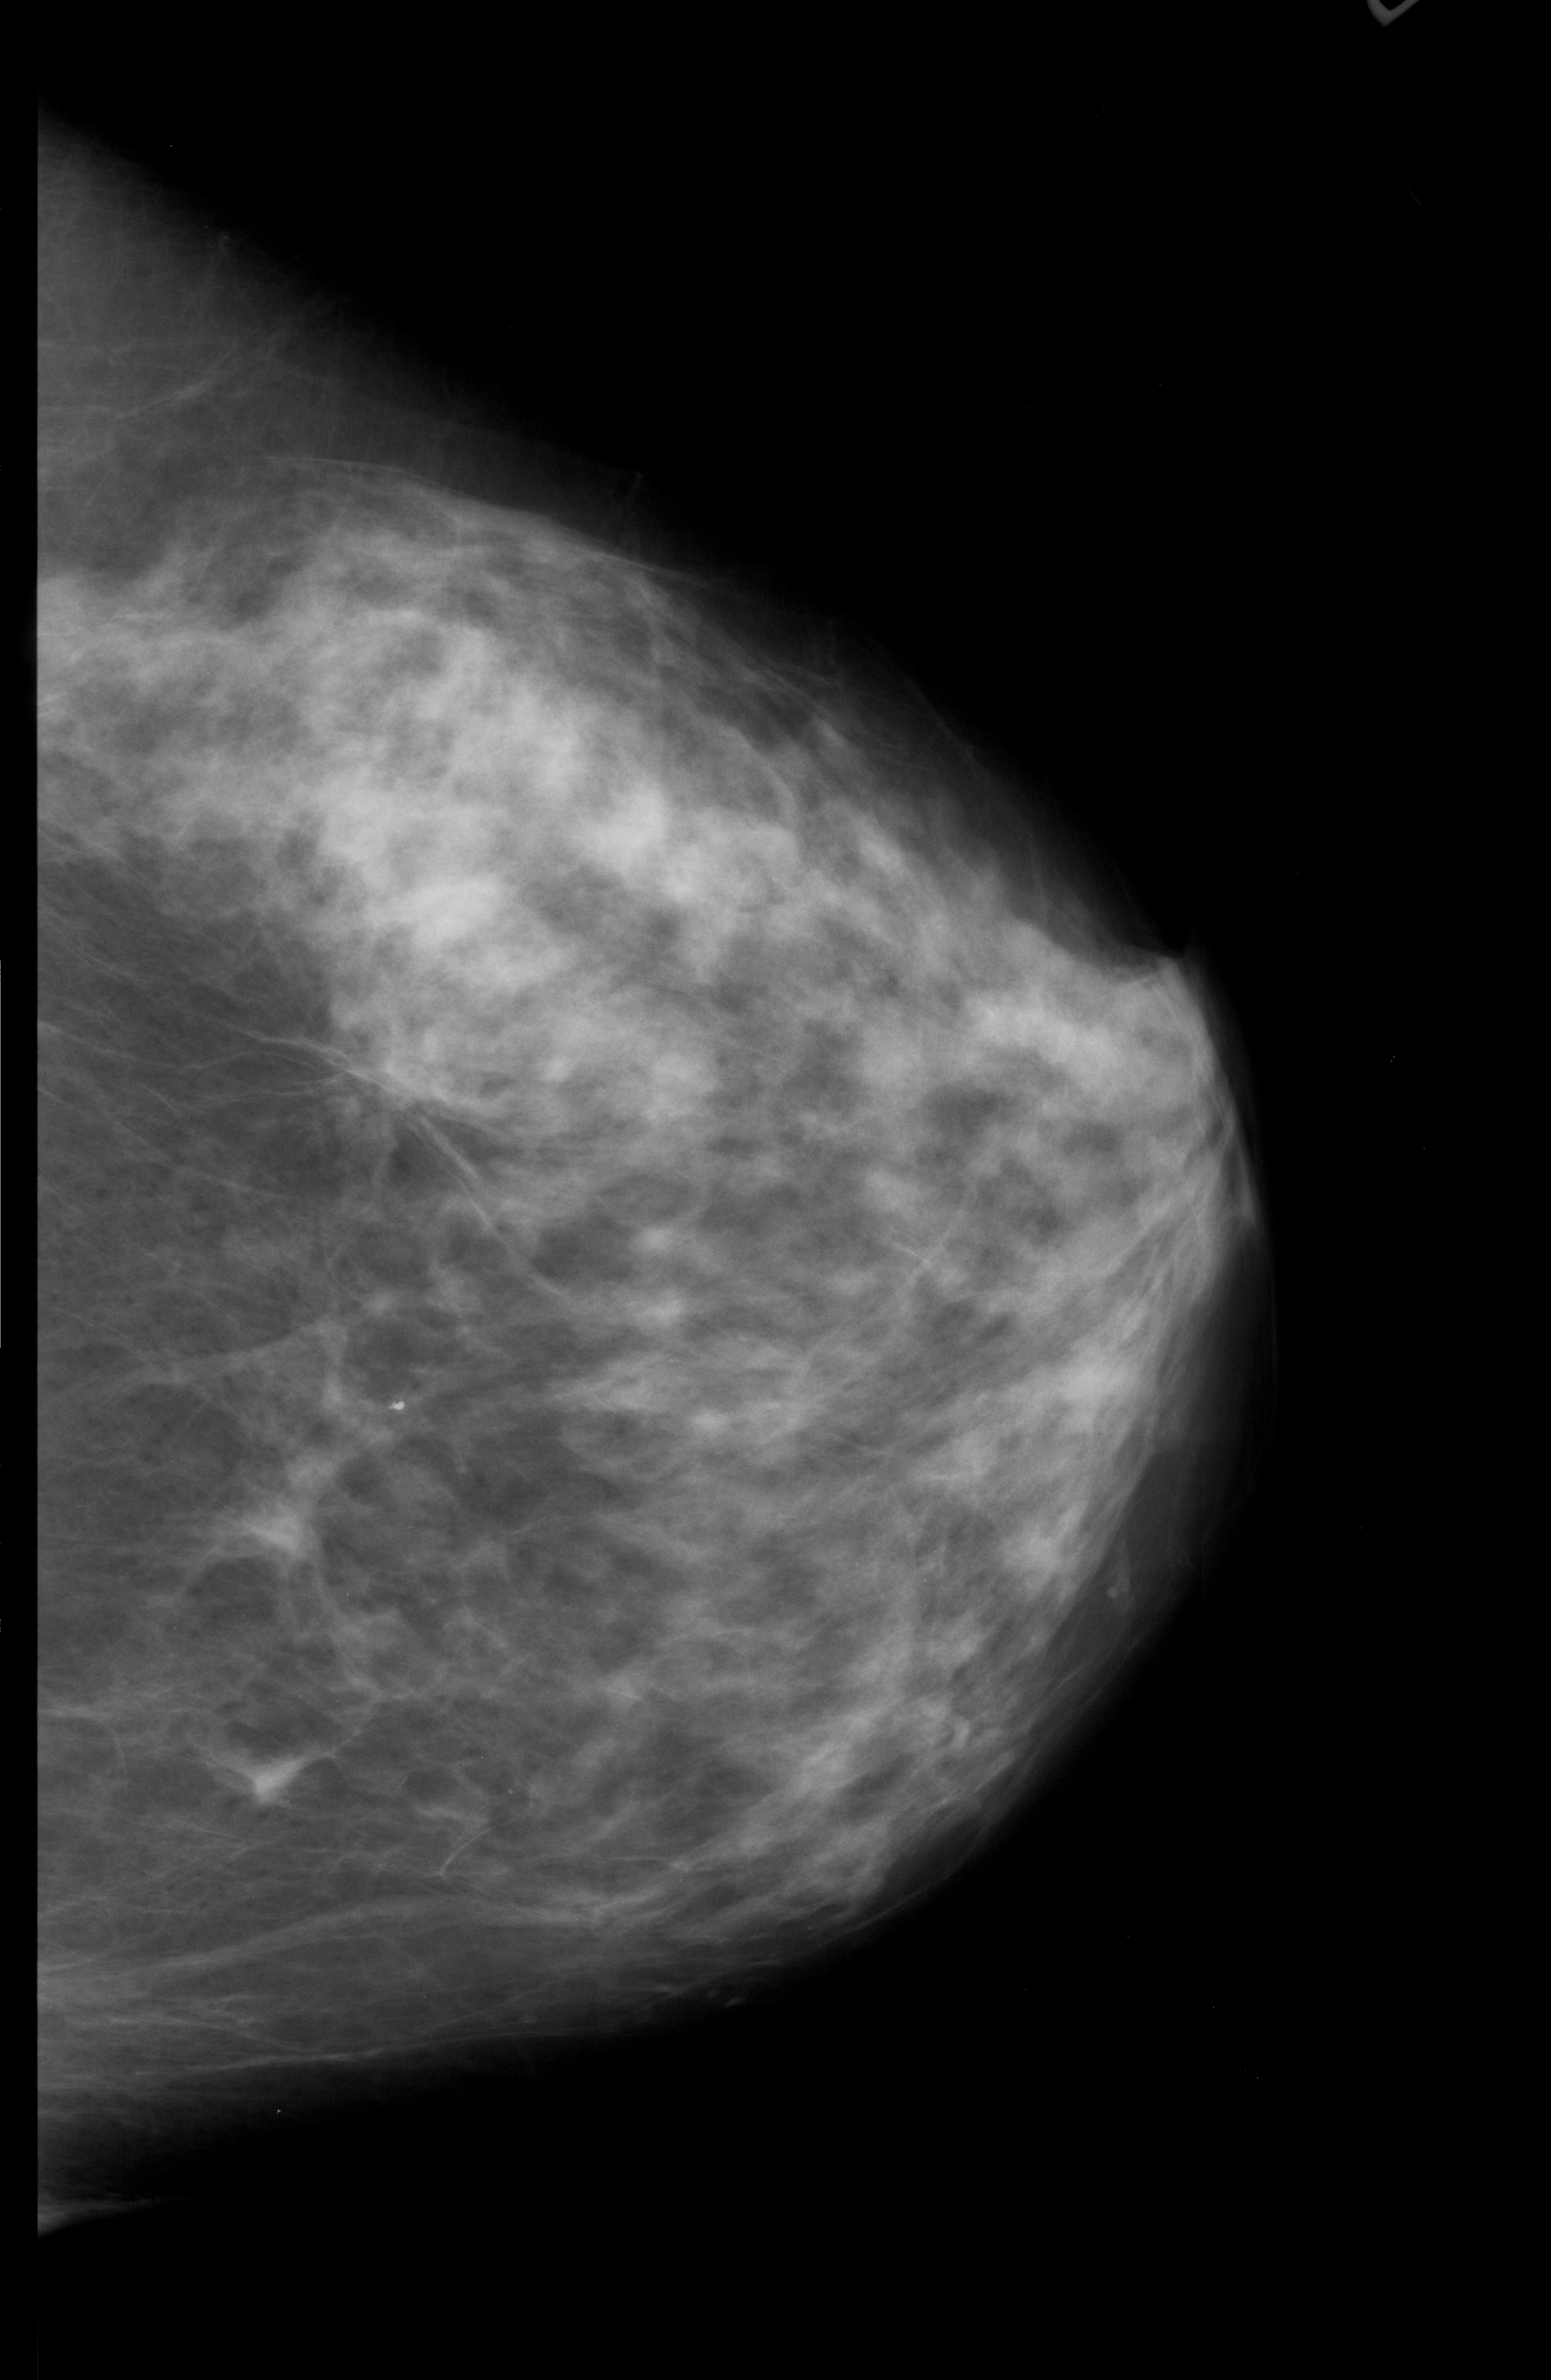
Digitized screen-film mammogram; right breast; CC view; BI-RADS breast density category 3 (scale 1–4); 1551 × 2380 image matrix.
Expert-marked regions of interest on this image (one box per marked abnormality):
- mass, shape architectural distortion, margins spiculated; BI-RADS assessment category 5; pathology (as recorded): malignant: box from (x=275, y=985) to (x=491, y=1156) px